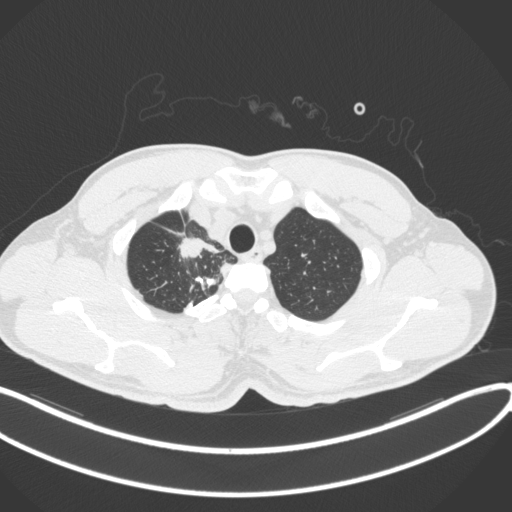
Chest CT, one axial slice; position 330 of 391 along the scan axis; 120 kVp; lung window (W 1500 / L -600 HU); 1 mm slice thickness; 512 × 512 image matrix, field of view 400 × 400 mm. Patient: male, 48 years. Case-level facts recorded for this patient, not image findings: clinical TNM (as recorded): T1c N1 M1.
Structures marked on this image (rectangle marked by the reading radiologist):
- lung tumour (recorded histology: adenocarcinoma): bounding box <177,236,224,264> (left, top, right, bottom; pixels)